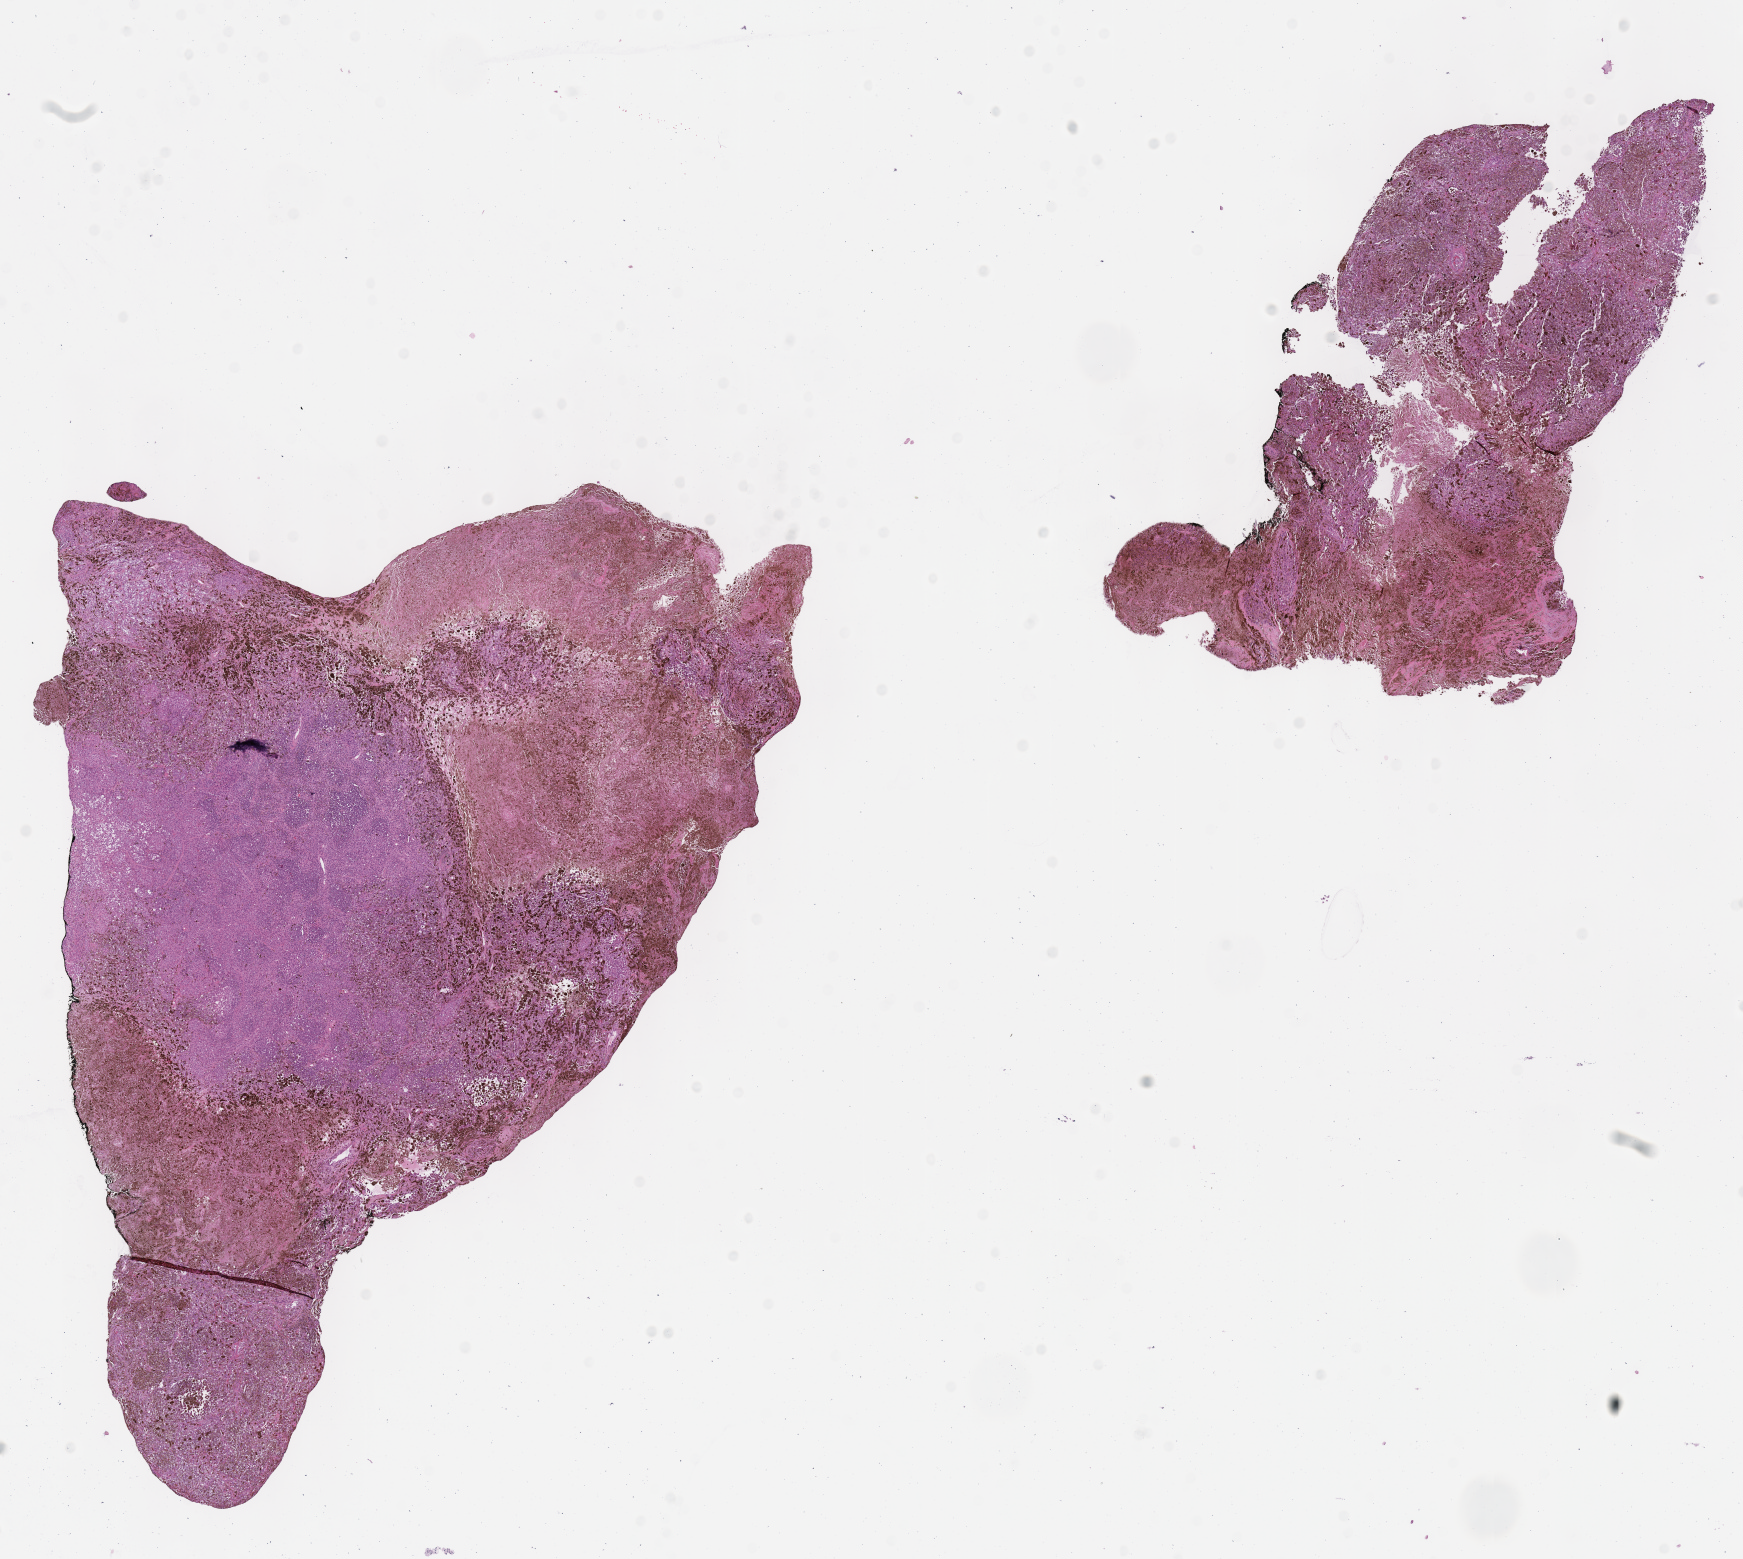
Whole-slide histology image, H&E-stained — low-resolution overview of the scanned area, about 13.7 x 12.3 mm (from a 40x scan), FFPE section, primary tumour sample from the skin. Female patient; age at initial diagnosis 72 years.
* histologic diagnosis: Malignant melanoma, NOS